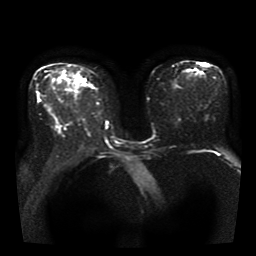
Breast MRI, one axial slice. Position 20 of 41 along the scan axis. Diffusion-weighted series; image 2 of 4 stored at this slice position (different b-values; order by instance number). 1.5 T. 256 × 256 image matrix, field of view 330 × 330 mm. Female patient.
Annotated regions visible in this slice (manually delineated by an expert):
- tumour on diffusion-weighted imaging: bounding box [x1, y1, x2, y2] px = [78, 76, 81, 80]